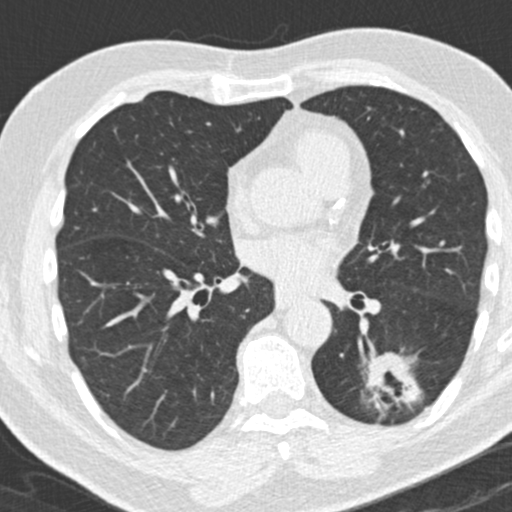
Chest CT (low-dose screening protocol), one axial image; third annual screen; lung window (W 1500 / L -600 HU); standard (soft-tissue) reconstruction kernel (B30f); slice 86 of 180 in the series; 512 × 512 image matrix, field of view 300 × 300 mm. Male participant, aged 66 years at enrolment. Former smoker at enrolment.
Lesion marked by an expert reader, bounding box <356,351,426,427> (left, top, right, bottom; pixels). The exam's reader record, not a measurement of the box and not confirmed to be the same lesion: non-calcified nodule or mass ≥4 mm, left lower lobe, 31 × 24 mm, spiculated (stellate) margins, pre-existing on the prior screen: yes; interval growth: yes. Official screen result: positive, other. Later outcome: lung cancer diagnosed 56 days after this screen — adenocarcinoma, NOS, left lower lobe, poorly differentiated (G3), stage IB (AJCC 6th edition), 38 mm at pathology.